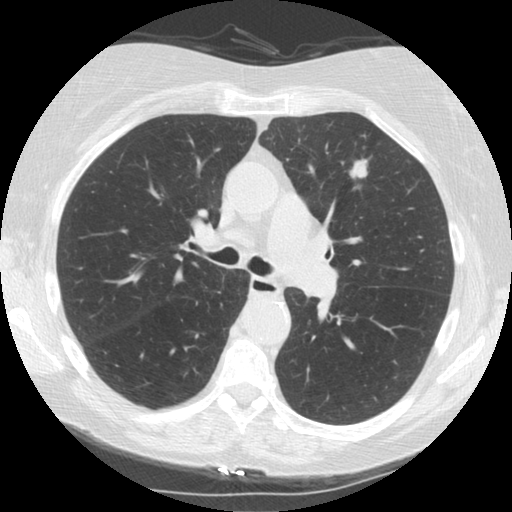
Low-dose screening chest CT, one axial slice. Slice 92 of 153 in the series (ordered by position). Reconstruction kernel STANDARD. 120 kVp. Lung window (W 1500 / L -600 HU). 2.5 mm slice thickness. 512 × 512 image matrix, field of view 330 × 330 mm.
Annotated regions visible in this slice (outlined manually by an expert reader):
- lesion 1 (tumor, upper lobe of left lung): bounding box <350,160,367,178> (left, top, right, bottom; pixels)